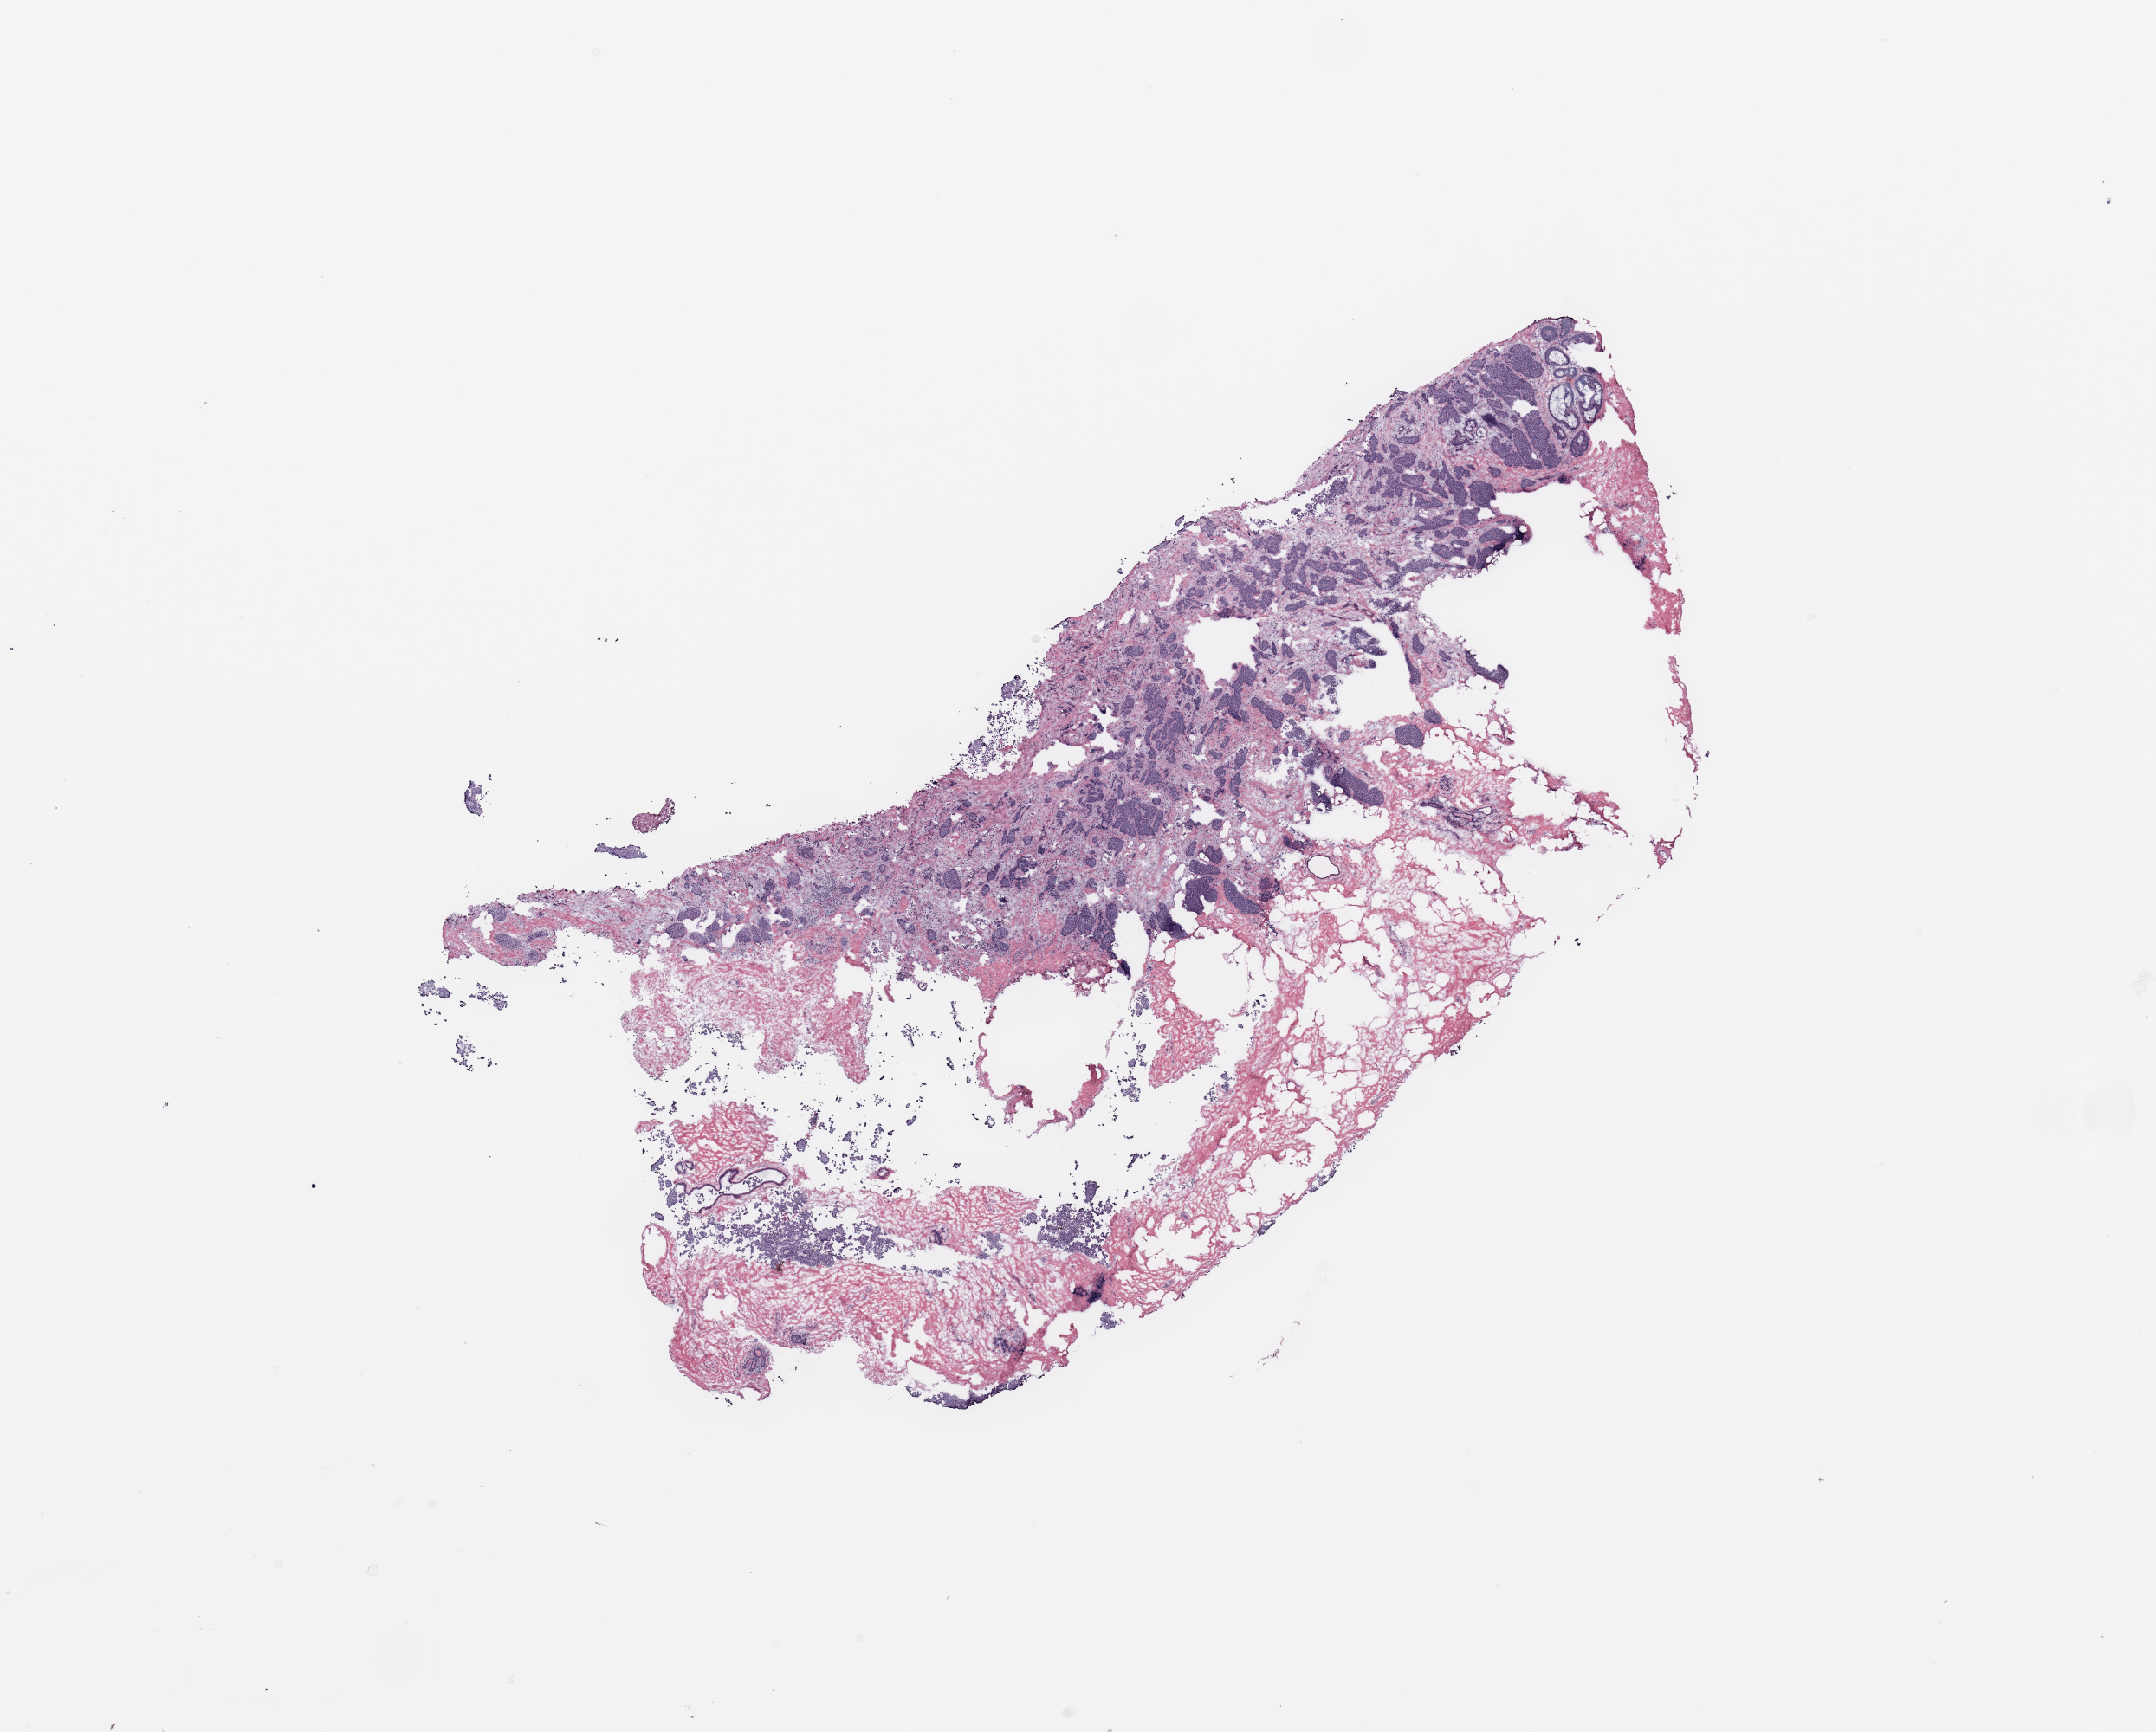
Whole-slide histology image, H&E-stained — a low-resolution overview of the entire scanned area, about 19.7 x 15.8 mm, breast, tissue type not recorded.
Patient diagnosis (cohort enrolment): breast cancer (breast).